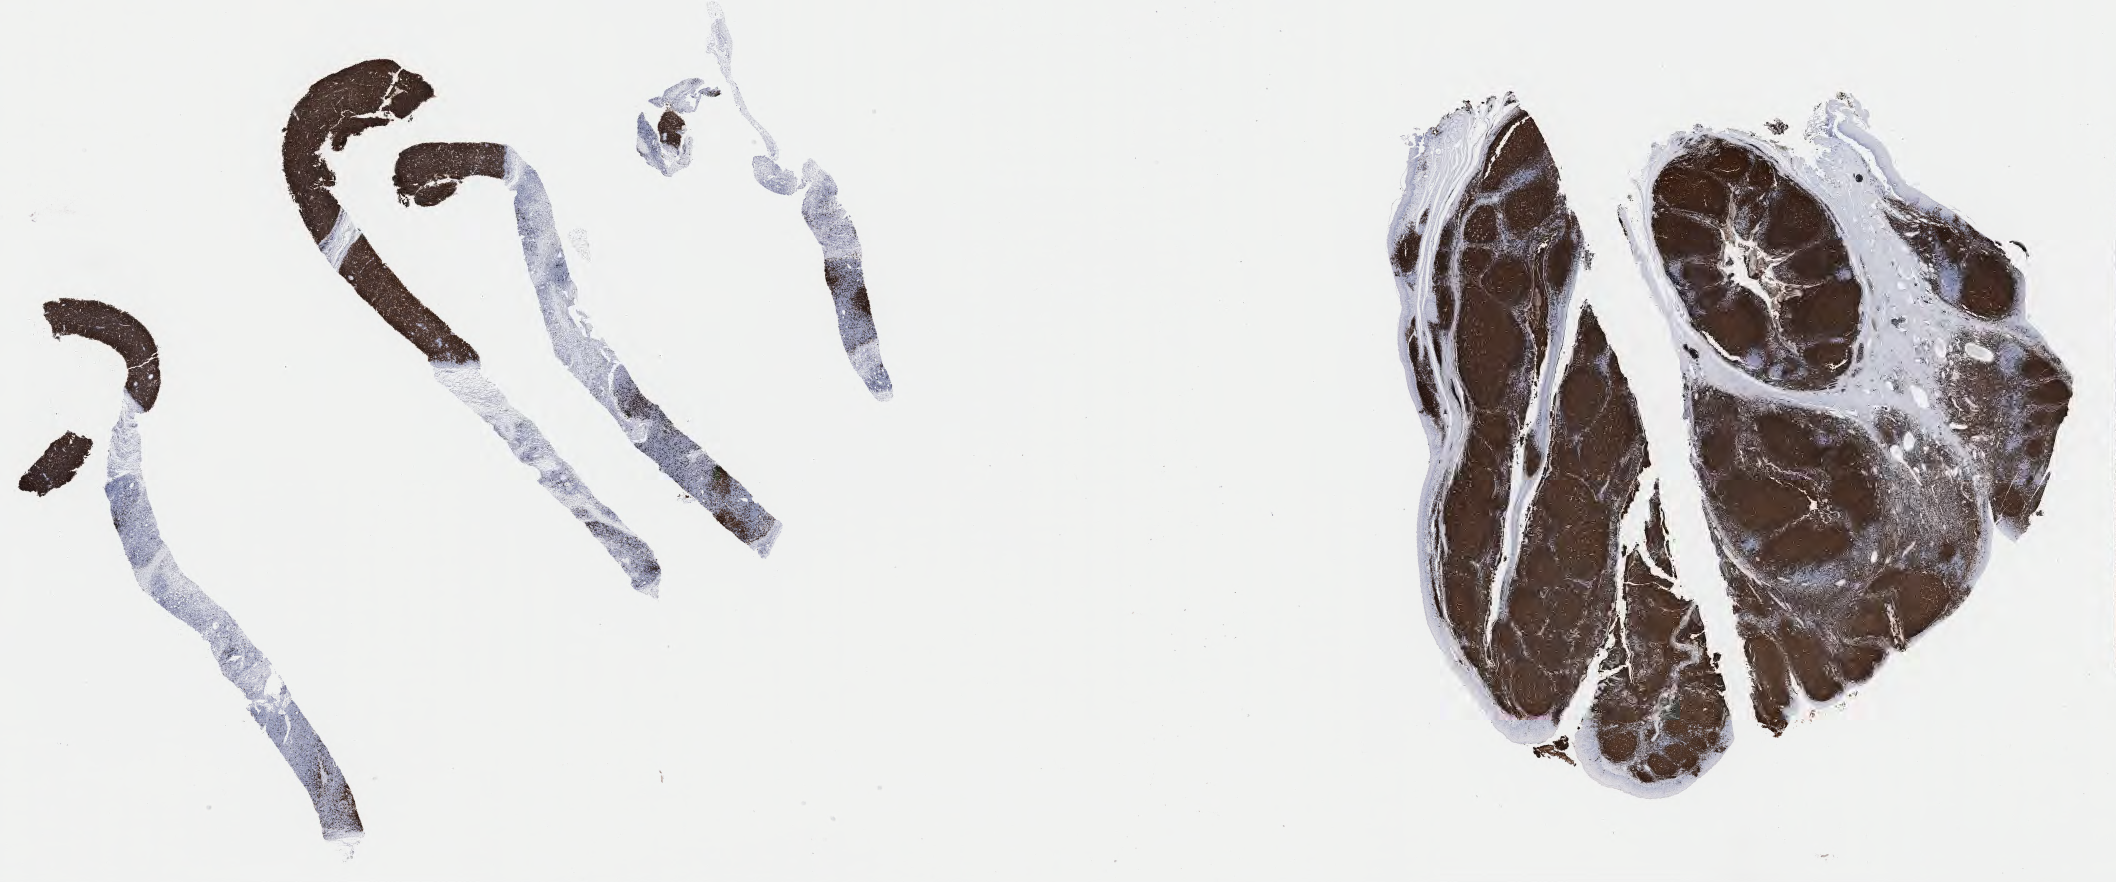
IHC for CD20, whole-slide image, shown as a low-resolution overview of the whole scanned area (about 34.2 x 14.3 mm), tumor tissue. Patient male; 47 years old.
Diagnosis: Burkitt lymphoma, NOS.